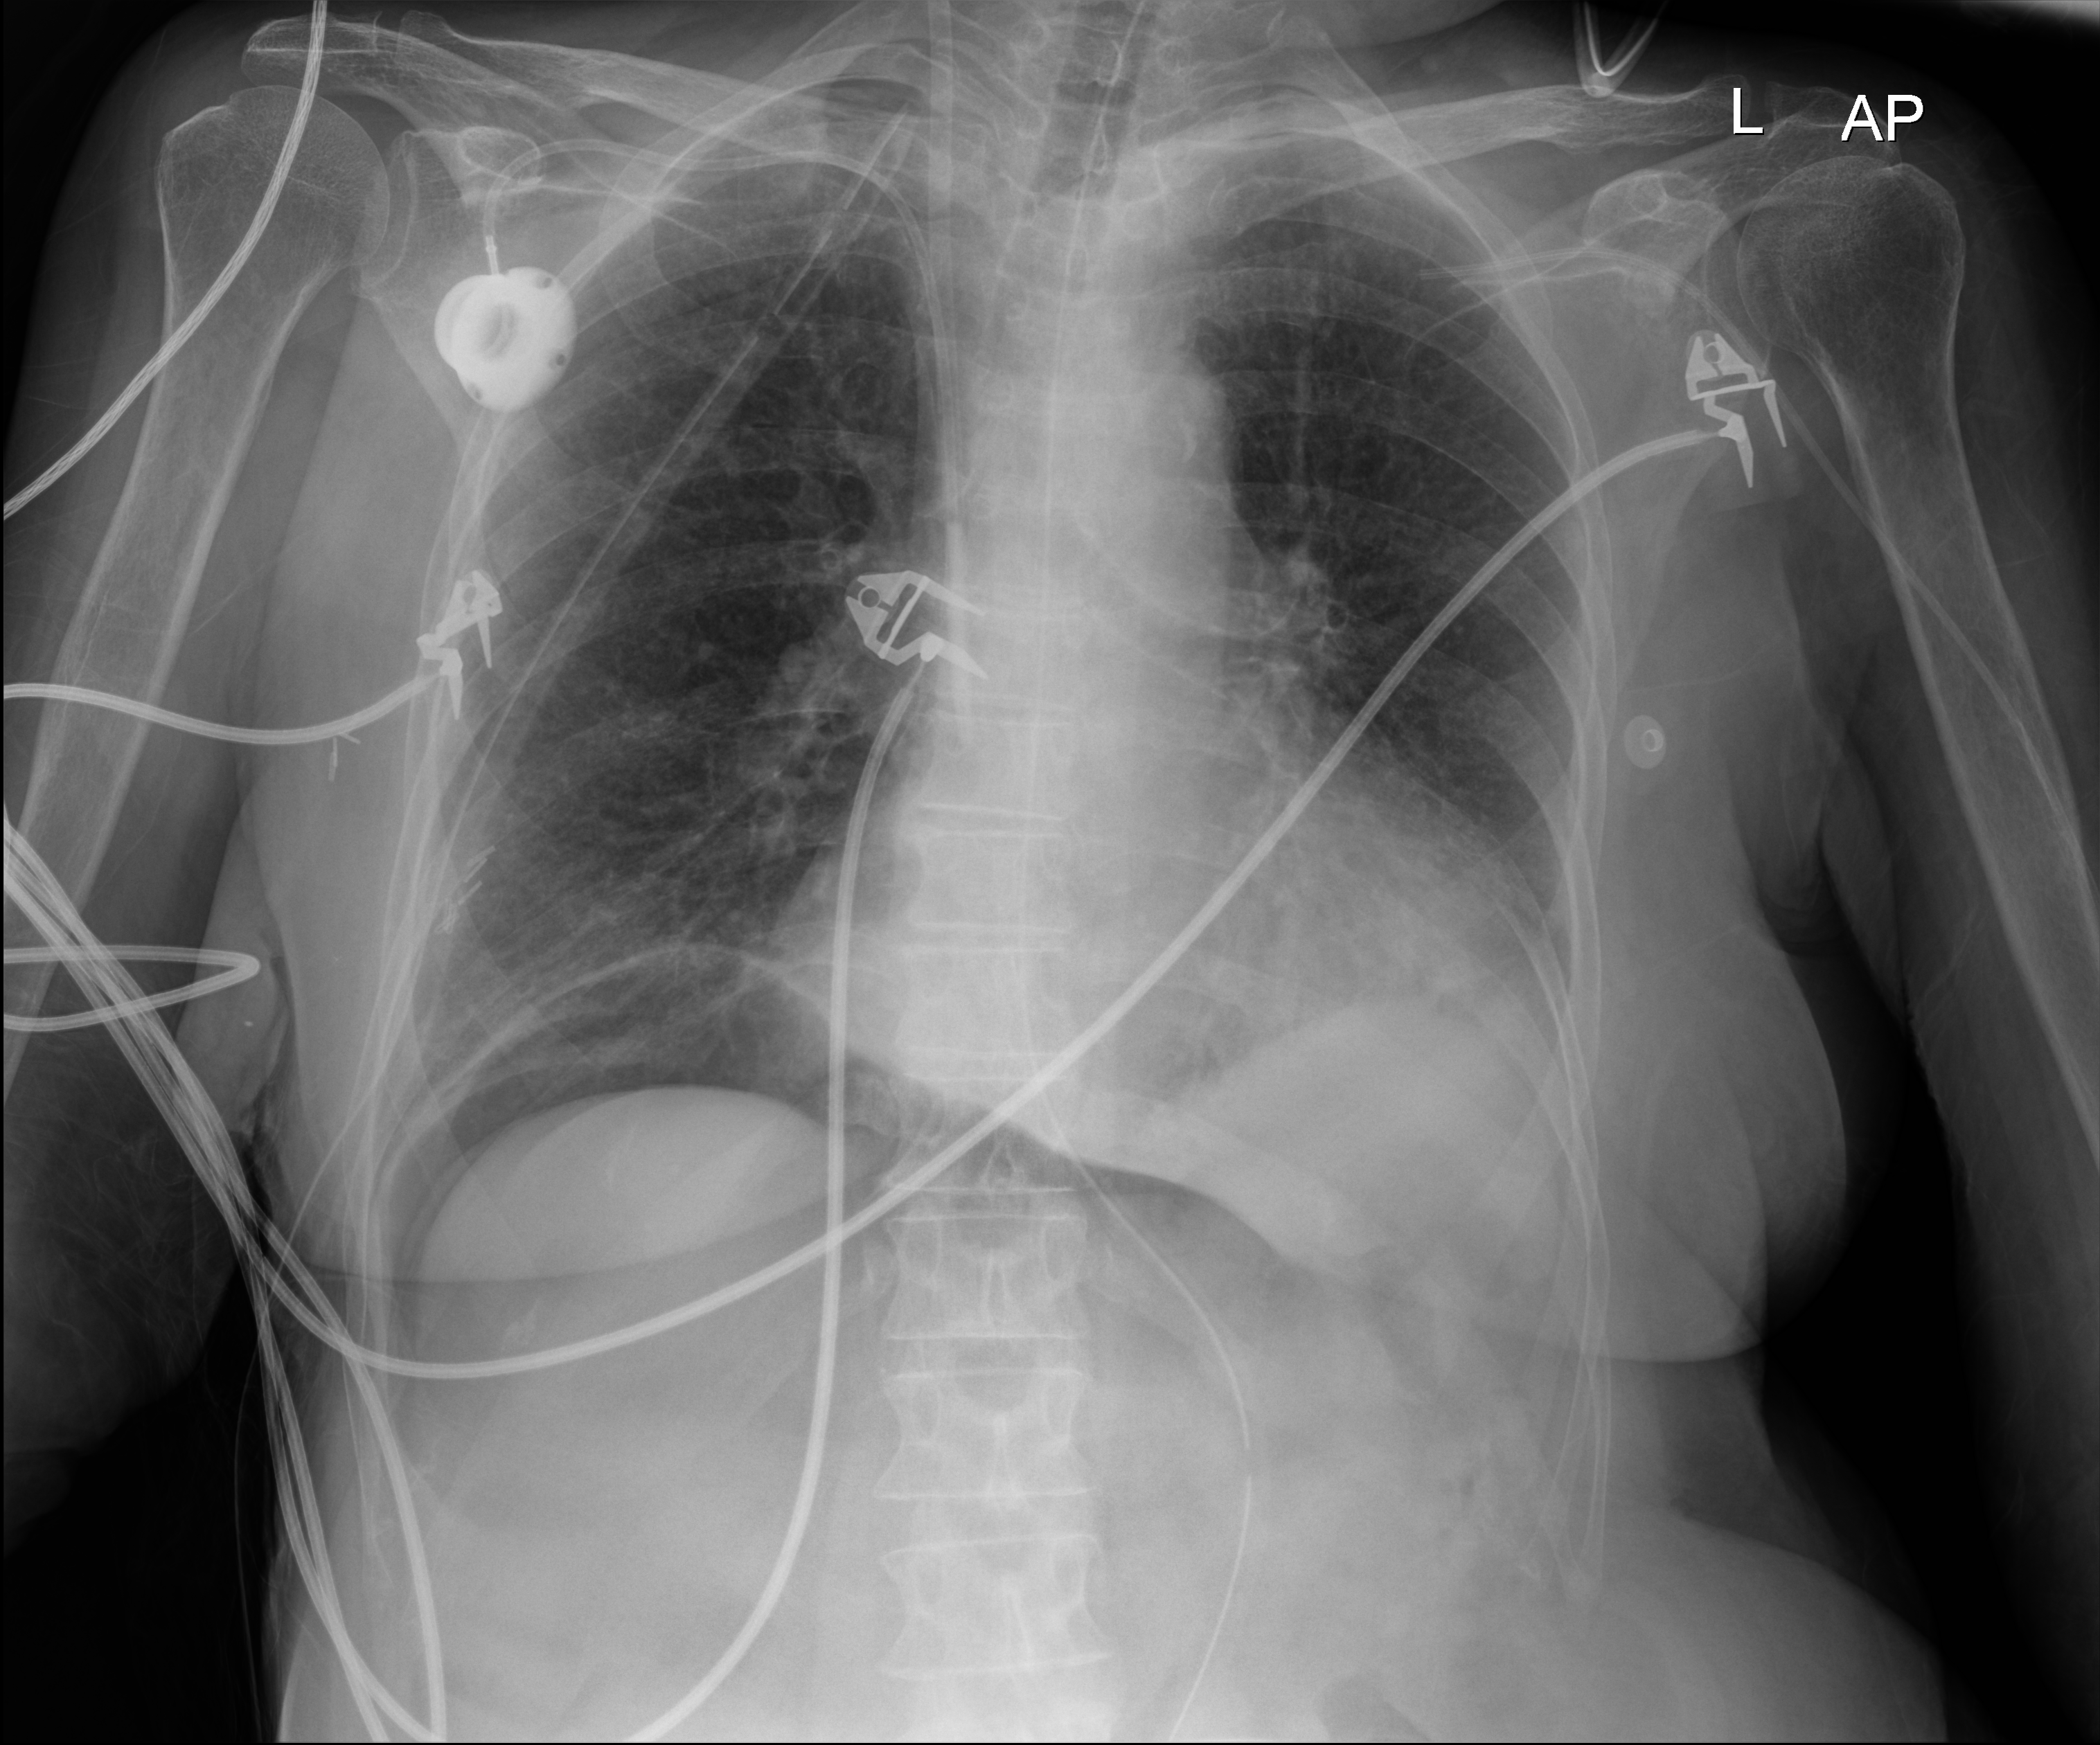
Chest X-ray (portable), anteroposterior (AP) projection. Female patient hospitalised with COVID-19, age 60–74 years.
Hospital-stay facts (about this admission, not read from this image; timing relative to this image not recorded): chronic kidney disease (admission record): no; diabetes (admission record): no; mechanically ventilated during this hospital stay: yes.